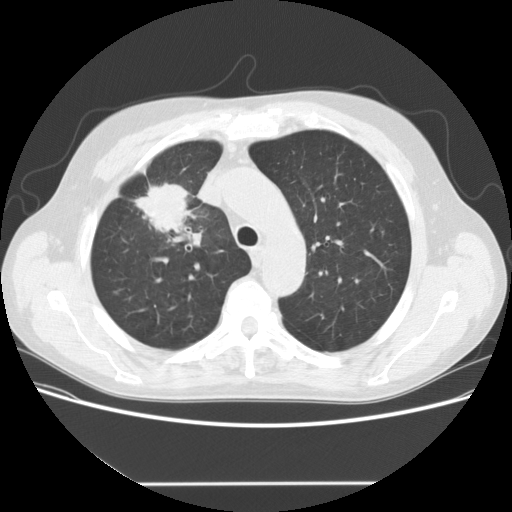
Axial slice from a low-dose chest CT screening exam. First (baseline) screen. Lung window (W 1500 / L -600 HU). Standard (soft-tissue) reconstruction kernel (STANDARD). 120 kVp. Slice 39 of 153 in the series. Male, age 56 years at enrolment. Current smoker at enrolment.
Expert-annotated lung lesion, box from (x=127, y=172) to (x=214, y=247) px. The screening reader recorded 2 non-calcified nodules or masses ≥4 mm on this exam (right upper lobe, right middle lobe); which of them this box marks is not recorded. Official screen result: positive, change unspecified: nodule(s) >= 4 mm or enlarging nodule(s), mass(es), or other non-specific abnormalities suspicious for lung cancer. Later outcome: lung cancer diagnosed 120 days after this screen — adenocarcinoma, NOS, right upper lobe, stage IIIA (AJCC 6th edition), 34 mm at pathology.